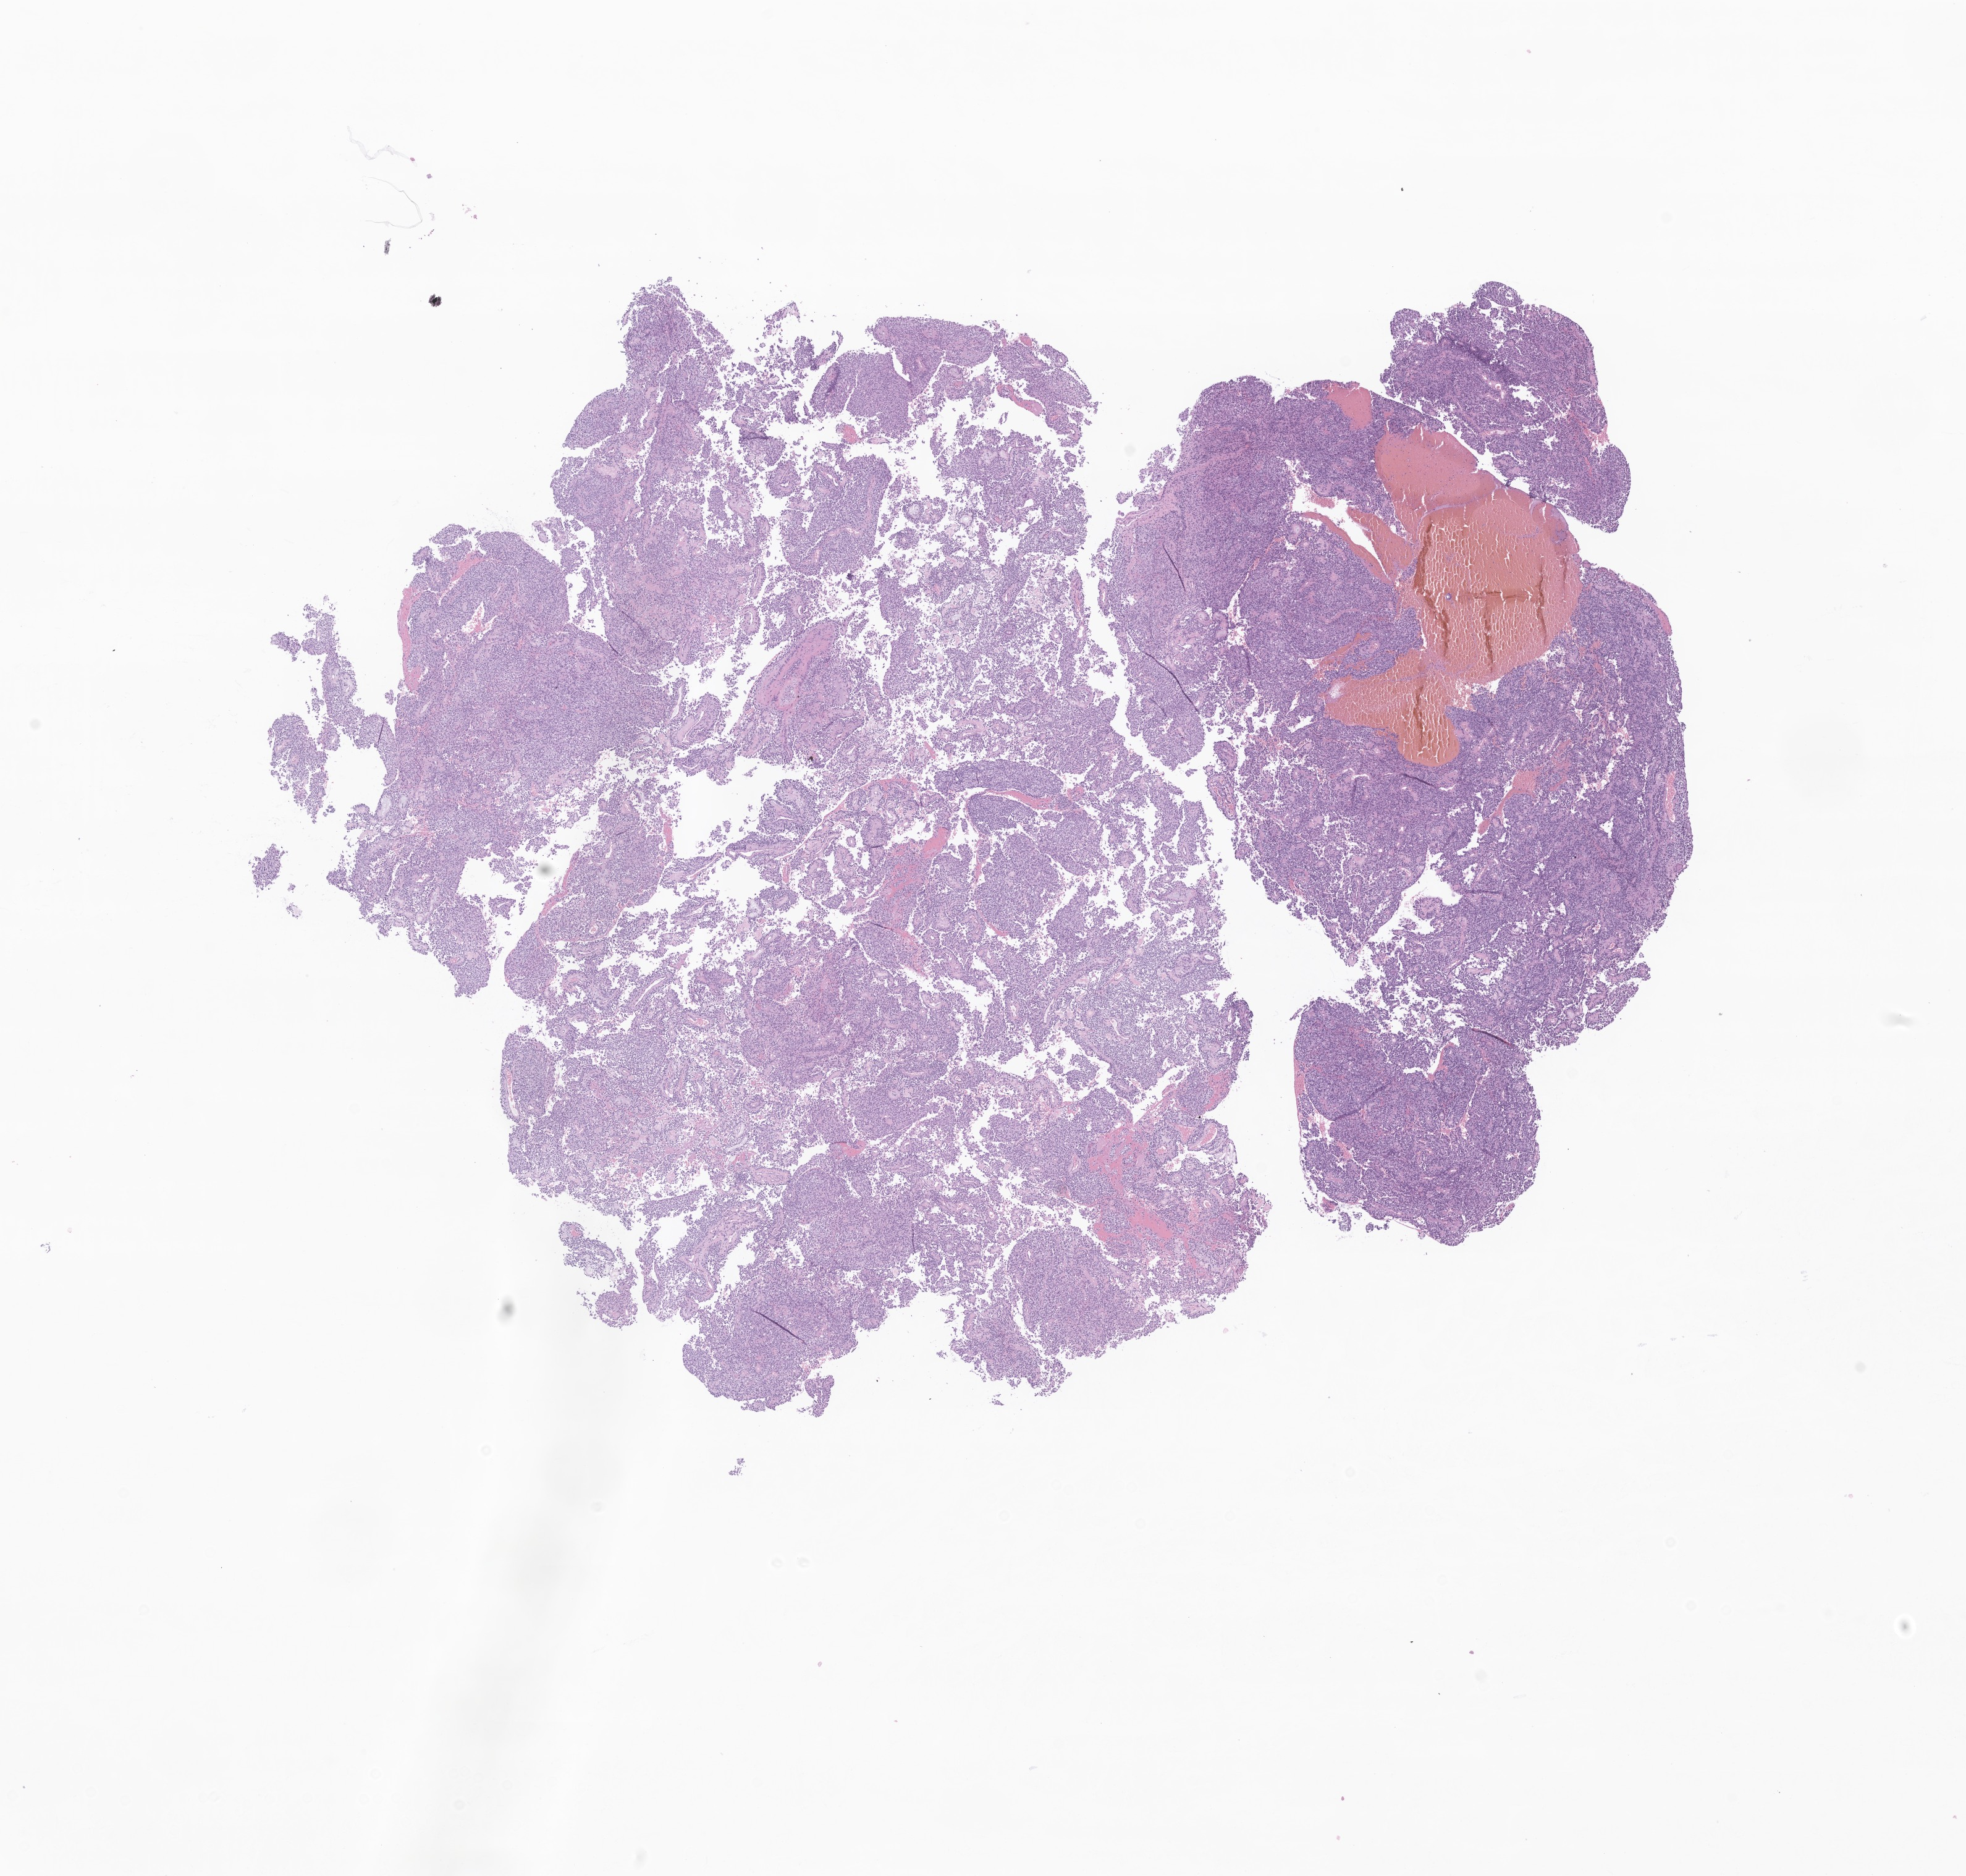
Hematoxylin and eosin (H&E) whole-slide image of tumor tissue from the brain — a low-resolution overview of the entire scanned area, about 13.4 x 12.8 mm; formalin-fixed paraffin-embedded section. Patient male; age 137 days.
* diagnosis: Neoplasm, uncertain whether benign or malignant